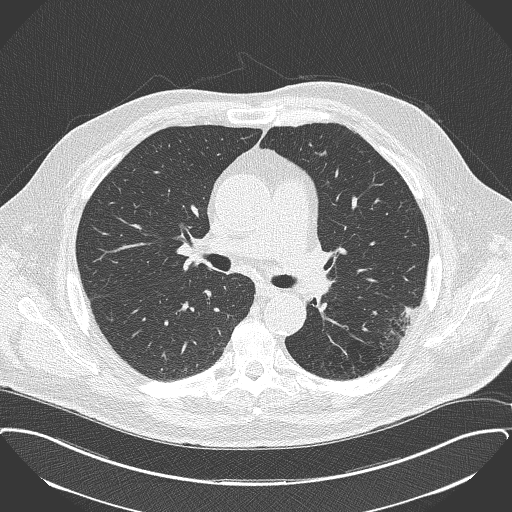
Chest CT (low-dose screening protocol), one axial image, second screening round (one year after baseline), lung window (W 1500 / L -600 HU), 2 mm slice thickness, lung (sharp) reconstruction kernel (B50f). Male participant, aged 68 years at enrolment.
Lesion marked by an expert reader, bounding box (x1, y1, x2, y2) in pixels: (370, 292, 428, 347). The screening reader recorded 2 non-calcified nodules or masses ≥4 mm on this exam (left lower lobe, left lower lobe); which of them this box marks is not recorded. Later outcome: lung cancer diagnosed 126 days after this screen — adenocarcinoma, NOS, left lower lobe, poorly differentiated (G3), stage IB (AJCC 6th edition), 17 mm at pathology.